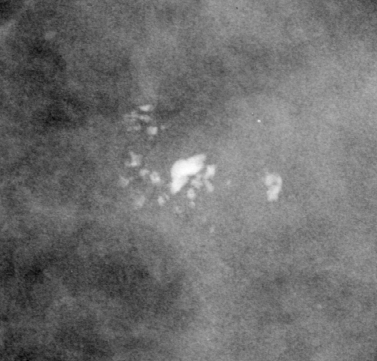
Cropped region of a digitized screen-film mammogram centred on a radiologist-marked abnormality, left breast, CC view.
Marked abnormality: calcifications, morphology pleomorphic, distribution clustered; BI-RADS assessment category 4; pathology (as recorded): benign.